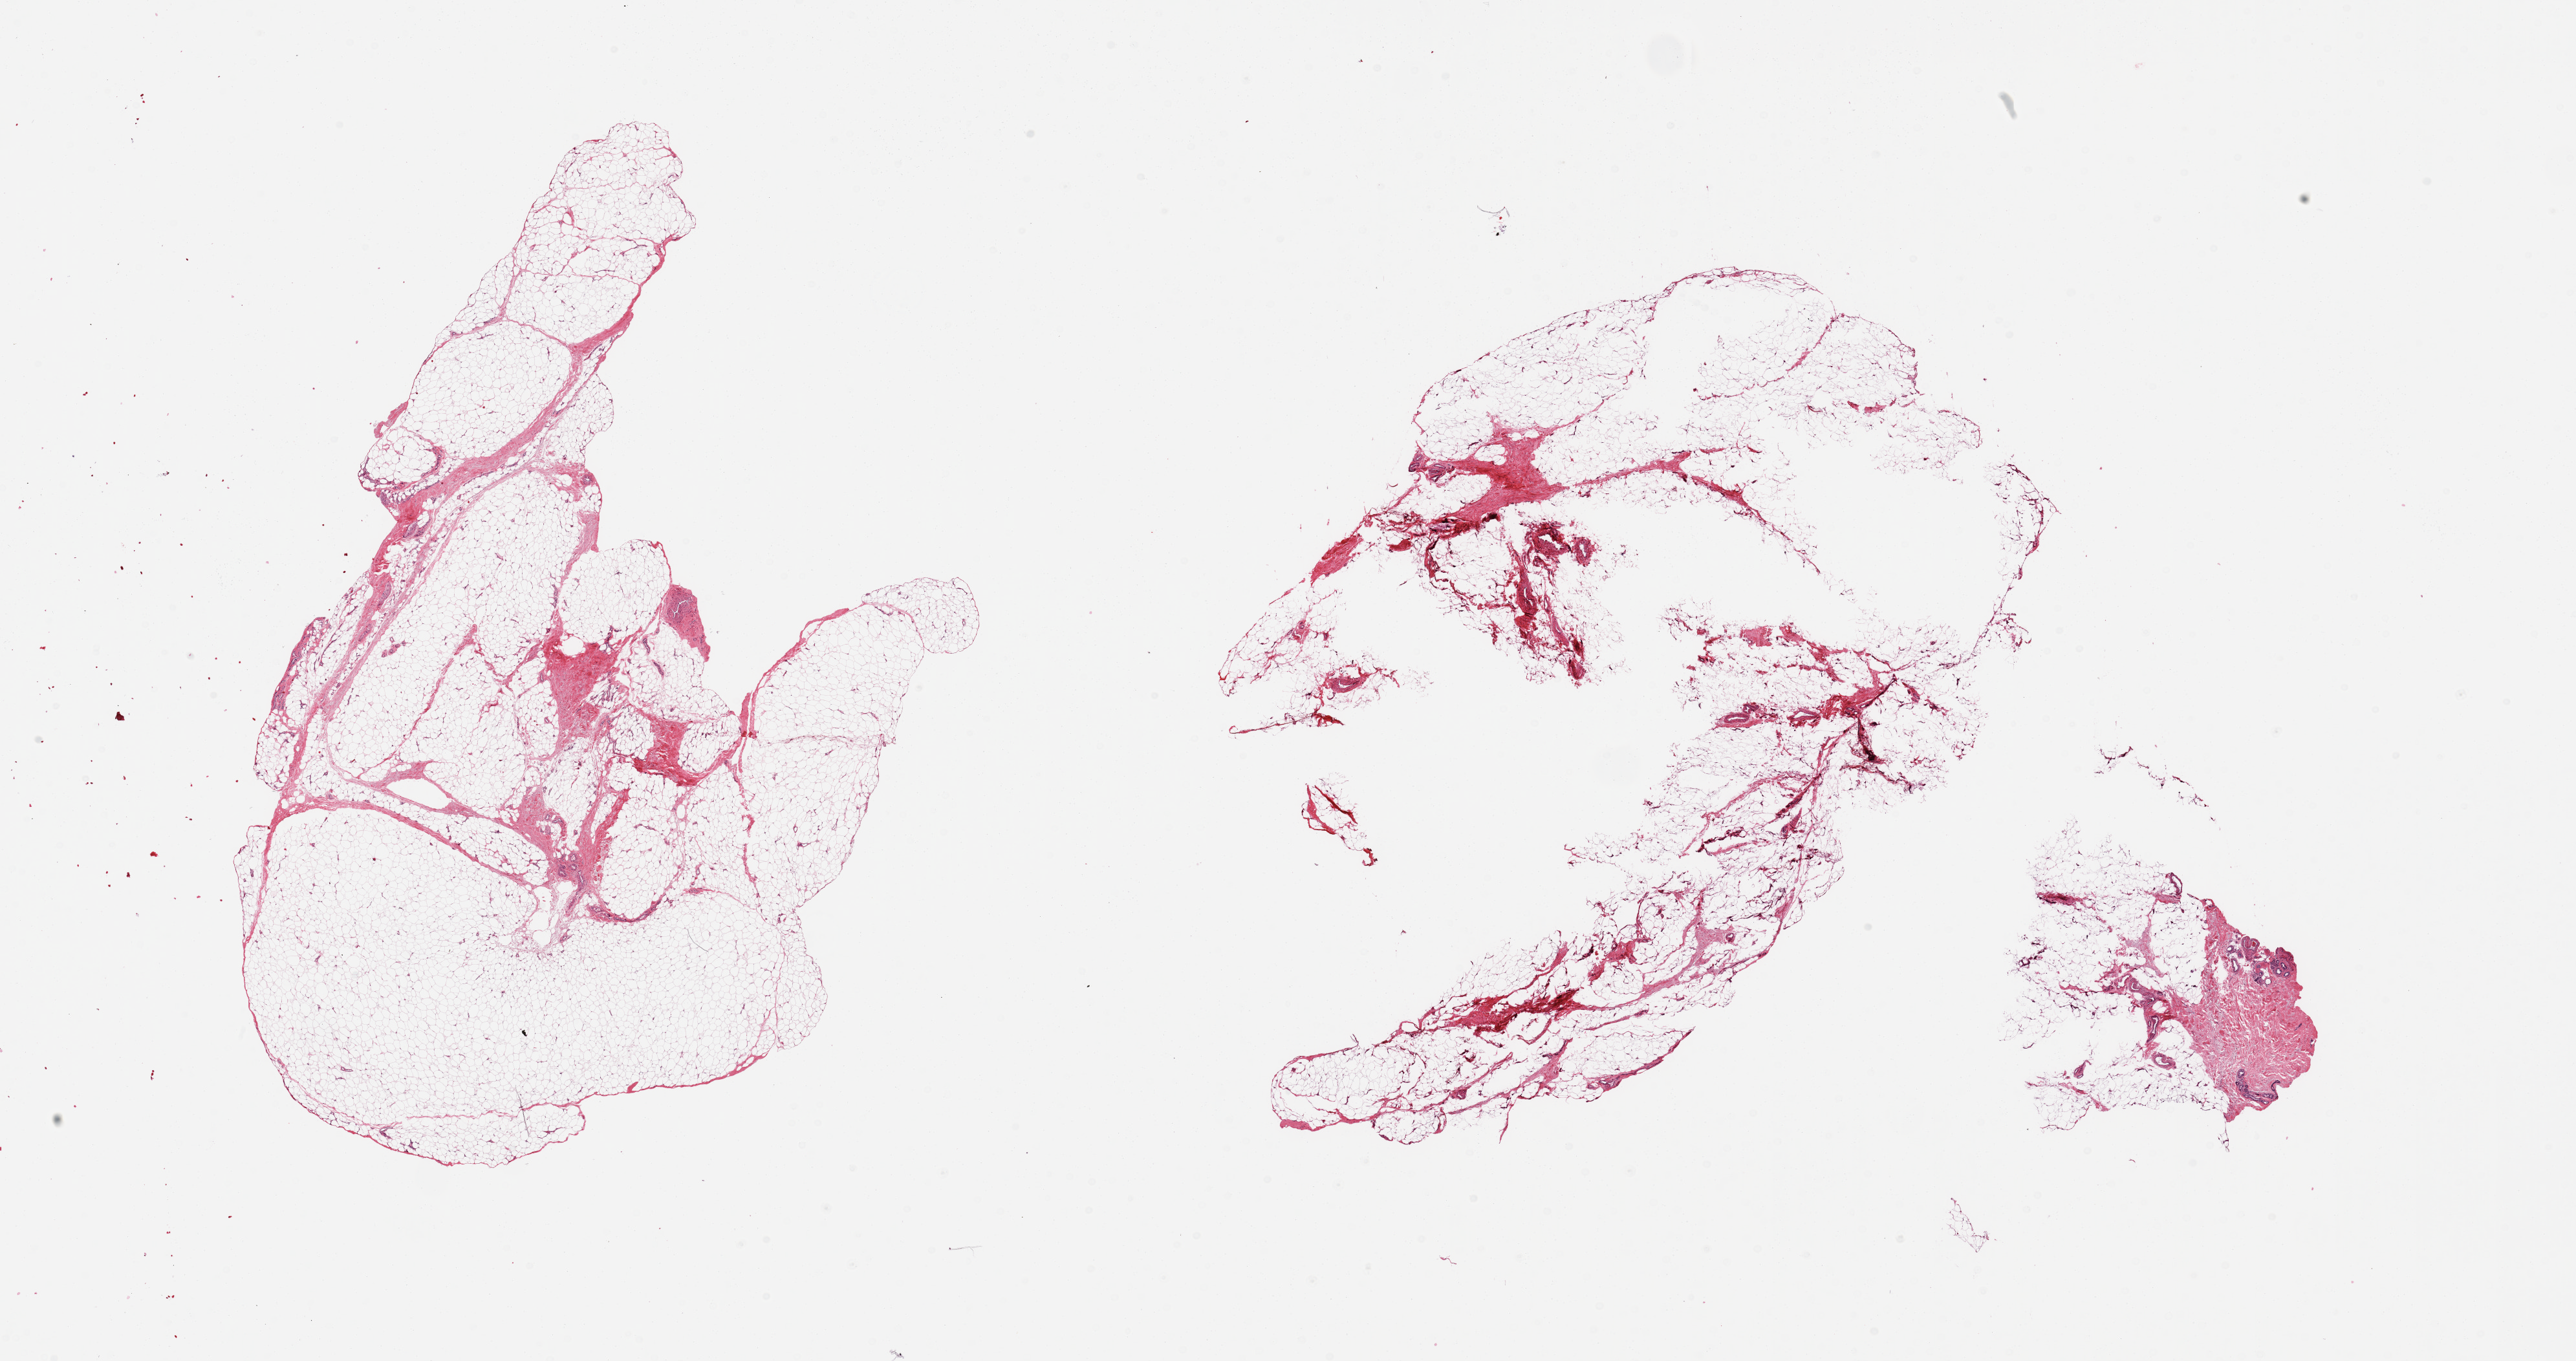
Whole-slide image, haematoxylin and eosin stain, shown as a low-resolution overview of the whole scanned area (about 31.5 x 16.6 mm), PAXgene-fixed paraffin-embedded (PFPE) section, section of adipose tissue (target tissue), tissue donor sample. Male donor.
Review note (as recorded): 2 pieces; includes ~10% fibrous tissue/sweat glands/nerve etc, 1 piece has large defect (?poor fixation).